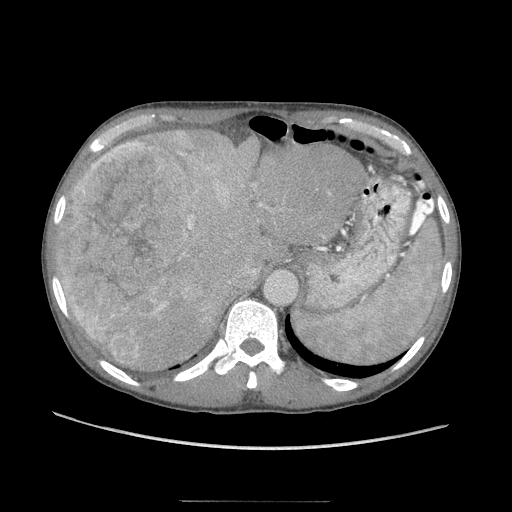
Contrast-enhanced abdominal CT (liver protocol), one axial slice. Slice 70 of 103 in the series (ordered by position). Reconstruction kernel STANDARD. Soft-tissue window (W 400 / L 40 HU). 2.5 mm slice thickness. 512 × 512 image matrix, field of view 380 × 380 mm. Case-level facts recorded for this patient, not image findings: diagnosis: hepatocellular carcinoma (patient treated with transarterial chemoembolisation; whether this scan precedes or follows treatment is not stated here); TNM stage (as recorded): Stage-IIIA; Child-Pugh class: A; tumour nodularity: multinodular.
Annotated regions visible in this slice (semi-automatically segmented with operator editing):
- liver parenchyma outside the tumour (the mass and vessels are separate outlines, so this box may not span the whole liver): bounding box (x1, y1, x2, y2) in pixels: (56, 128, 364, 368)
- mass: (59, 140, 192, 368)
- liver vessels: (156, 151, 201, 310)